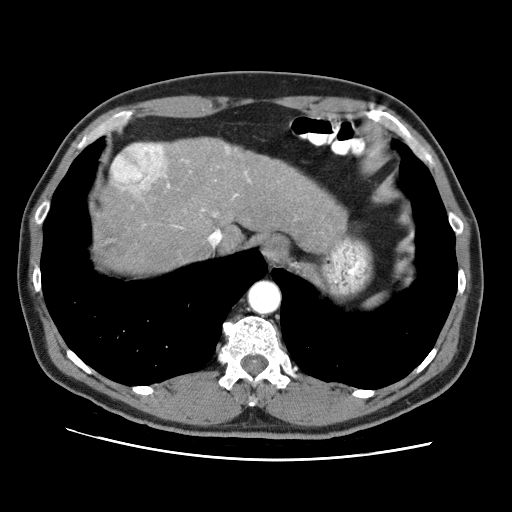
Contrast-enhanced abdominal CT (liver protocol), one axial slice; position 59 of 71 along the scan axis; 120 kVp; soft-tissue window (W 400 / L 40 HU); 512 × 512 image matrix, field of view 360 × 360 mm. From the clinical record (not read from this slice): diagnosis: hepatocellular carcinoma (patient treated with transarterial chemoembolisation; whether this scan precedes or follows treatment is not stated here); TNM stage (as recorded): Stage-II; Child-Pugh class: A; tumour size: 4.6 cm.
Annotated regions visible in this slice (semi-automatic segmentation, software-assisted and operator-edited):
- liver parenchyma outside the tumour (the mass and vessels are separate outlines, so this box may not span the whole liver): box from (x=94, y=138) to (x=346, y=272) px
- mass: (x=111, y=143)–(x=171, y=193)
- liver vessels: (x=167, y=185)–(x=237, y=196)